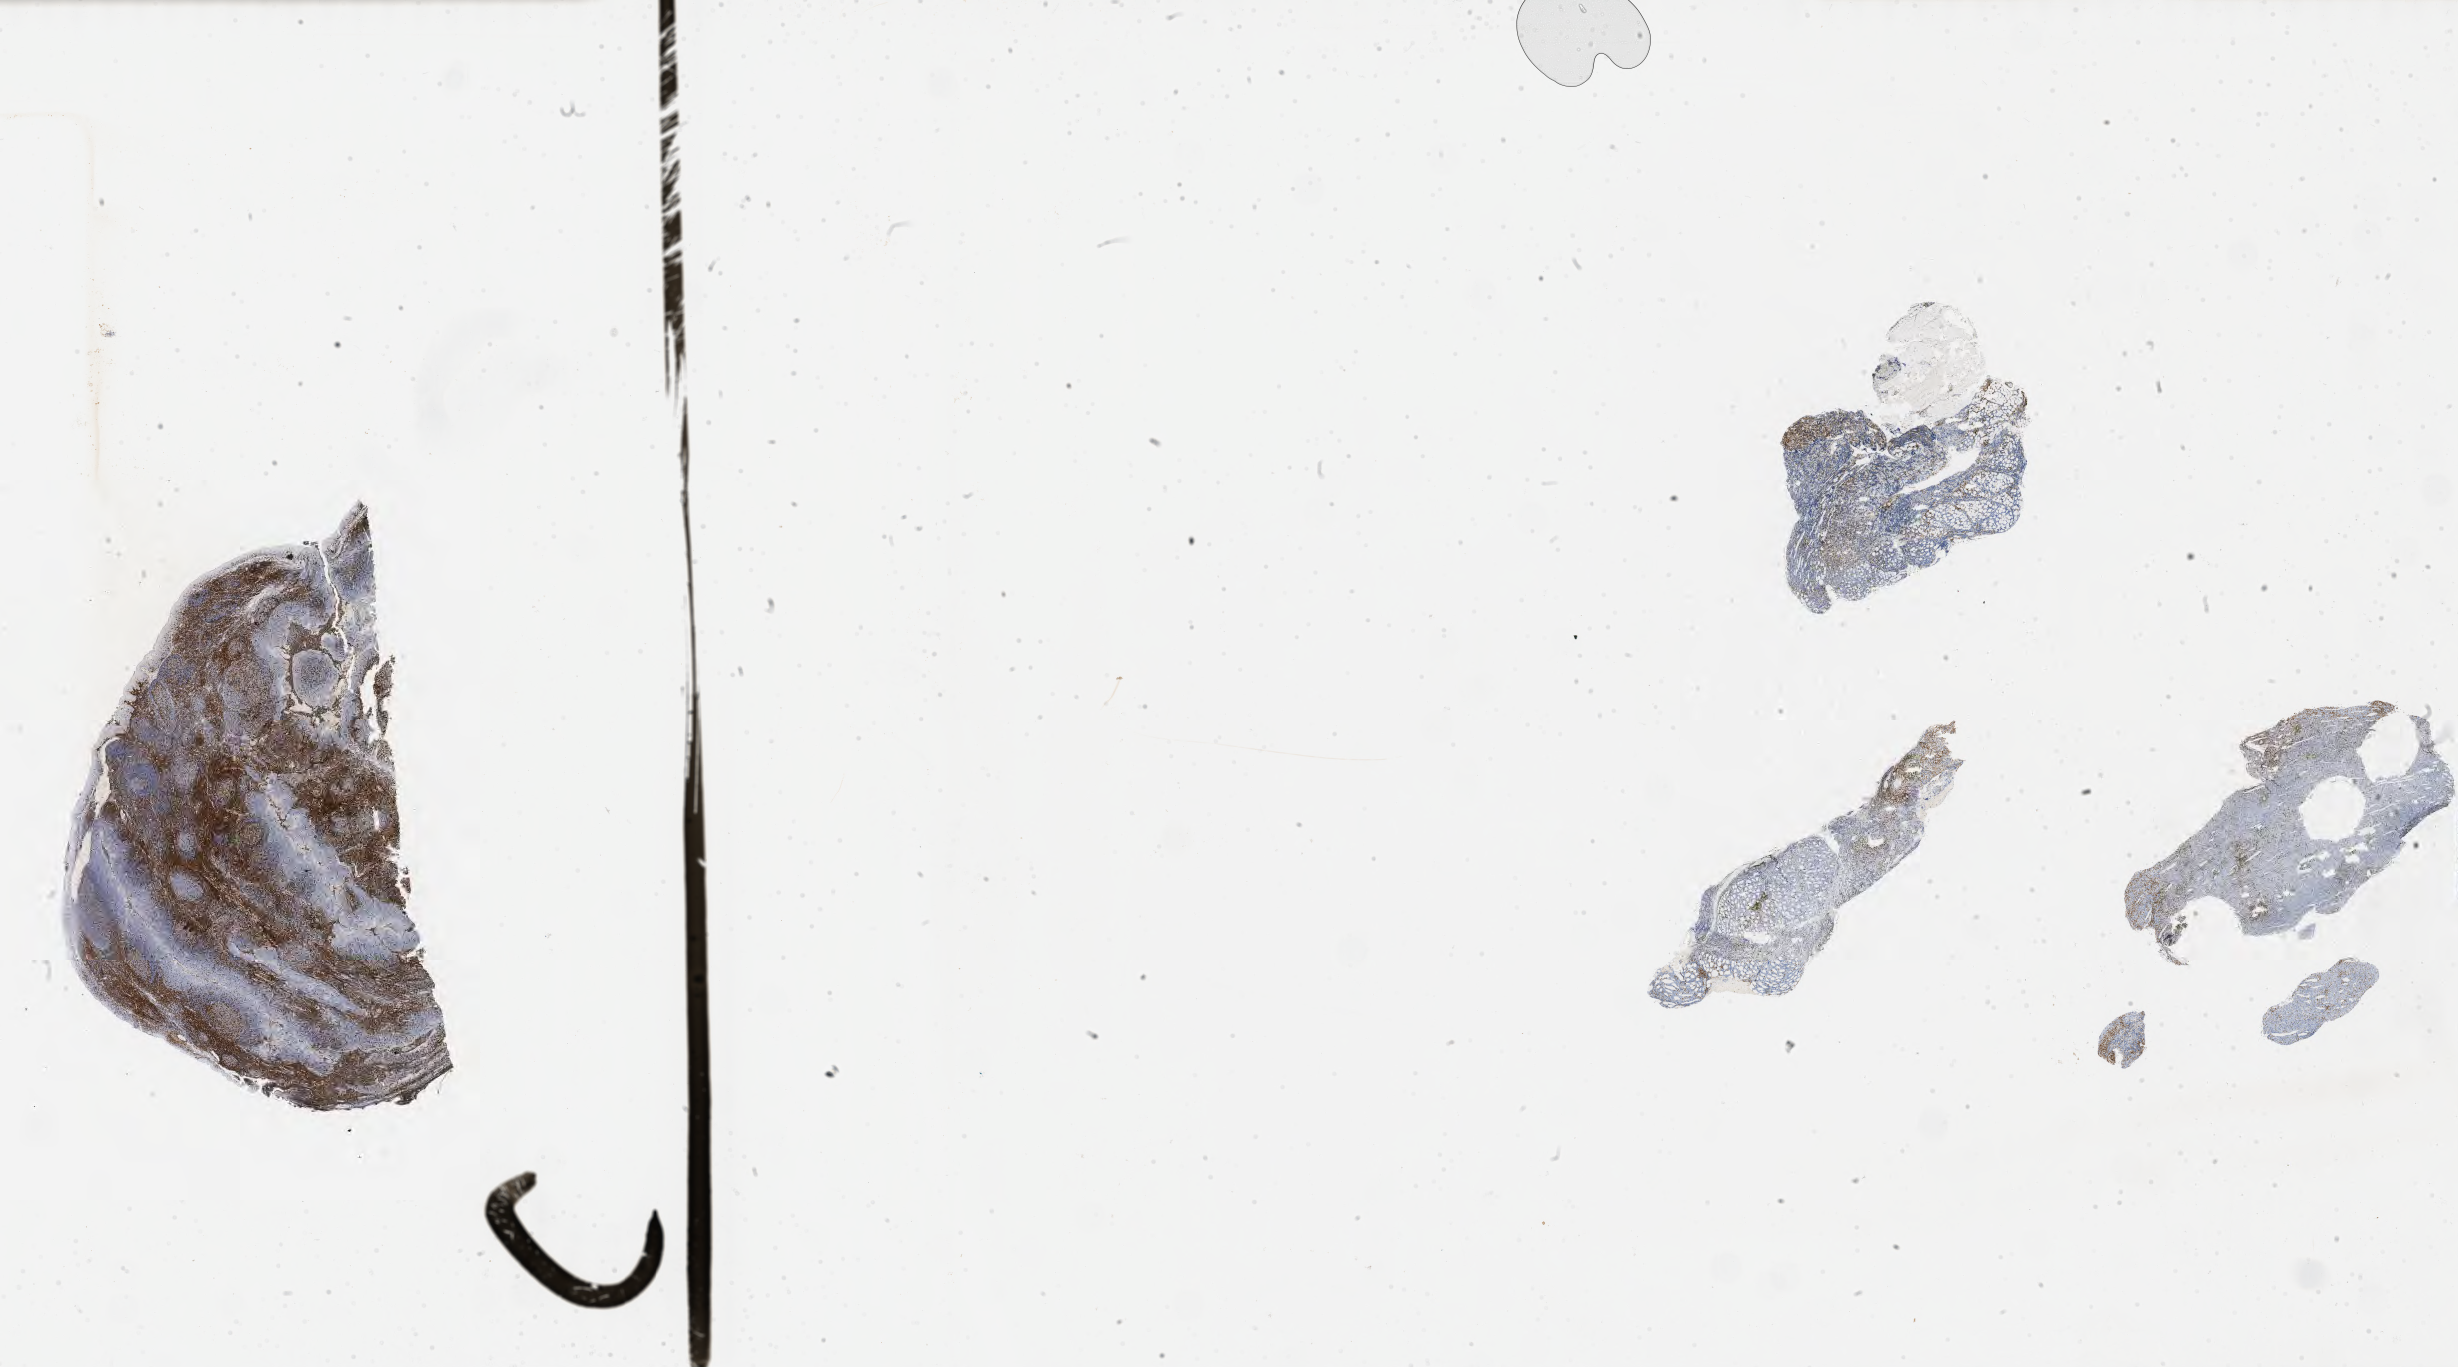
Whole-slide image, immunohistochemical stain for CD3, a low-resolution overview of the entire scanned area, about 39.8 x 22.1 mm; specimen: tumor tissue; anatomic site: lymph node of head and neck. Male patient, aged 55.
Histologic diagnosis: Burkitt lymphoma, NOS.